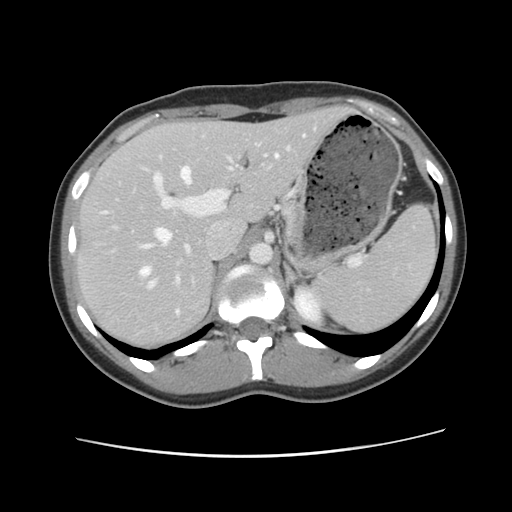
Contrast-enhanced abdominal CT, one axial slice; position 75 of 134 along the scan axis; intravenous contrast given; soft-tissue window (W 400 / L 40 HU); 512 × 512 image matrix, field of view 339 × 339 mm. Female patient, age 33 years. Case-level facts recorded for this patient, not image findings: diagnosis: colorectal cancer liver metastases, imaged before liver resection; multiple liver metastases: yes; largest metastasis: 4.5 cm.
Annotated regions visible in this slice (outlined manually by an expert reader):
- hepatic veins: box from (x=105, y=154) to (x=279, y=314) px
- liver: (x=78, y=108)–(x=348, y=350)
- planned liver remnant (the part of the liver to remain after resection): (x=78, y=108)–(x=349, y=350)
- portal vein (with intrahepatic branches): (x=151, y=145)–(x=293, y=285)